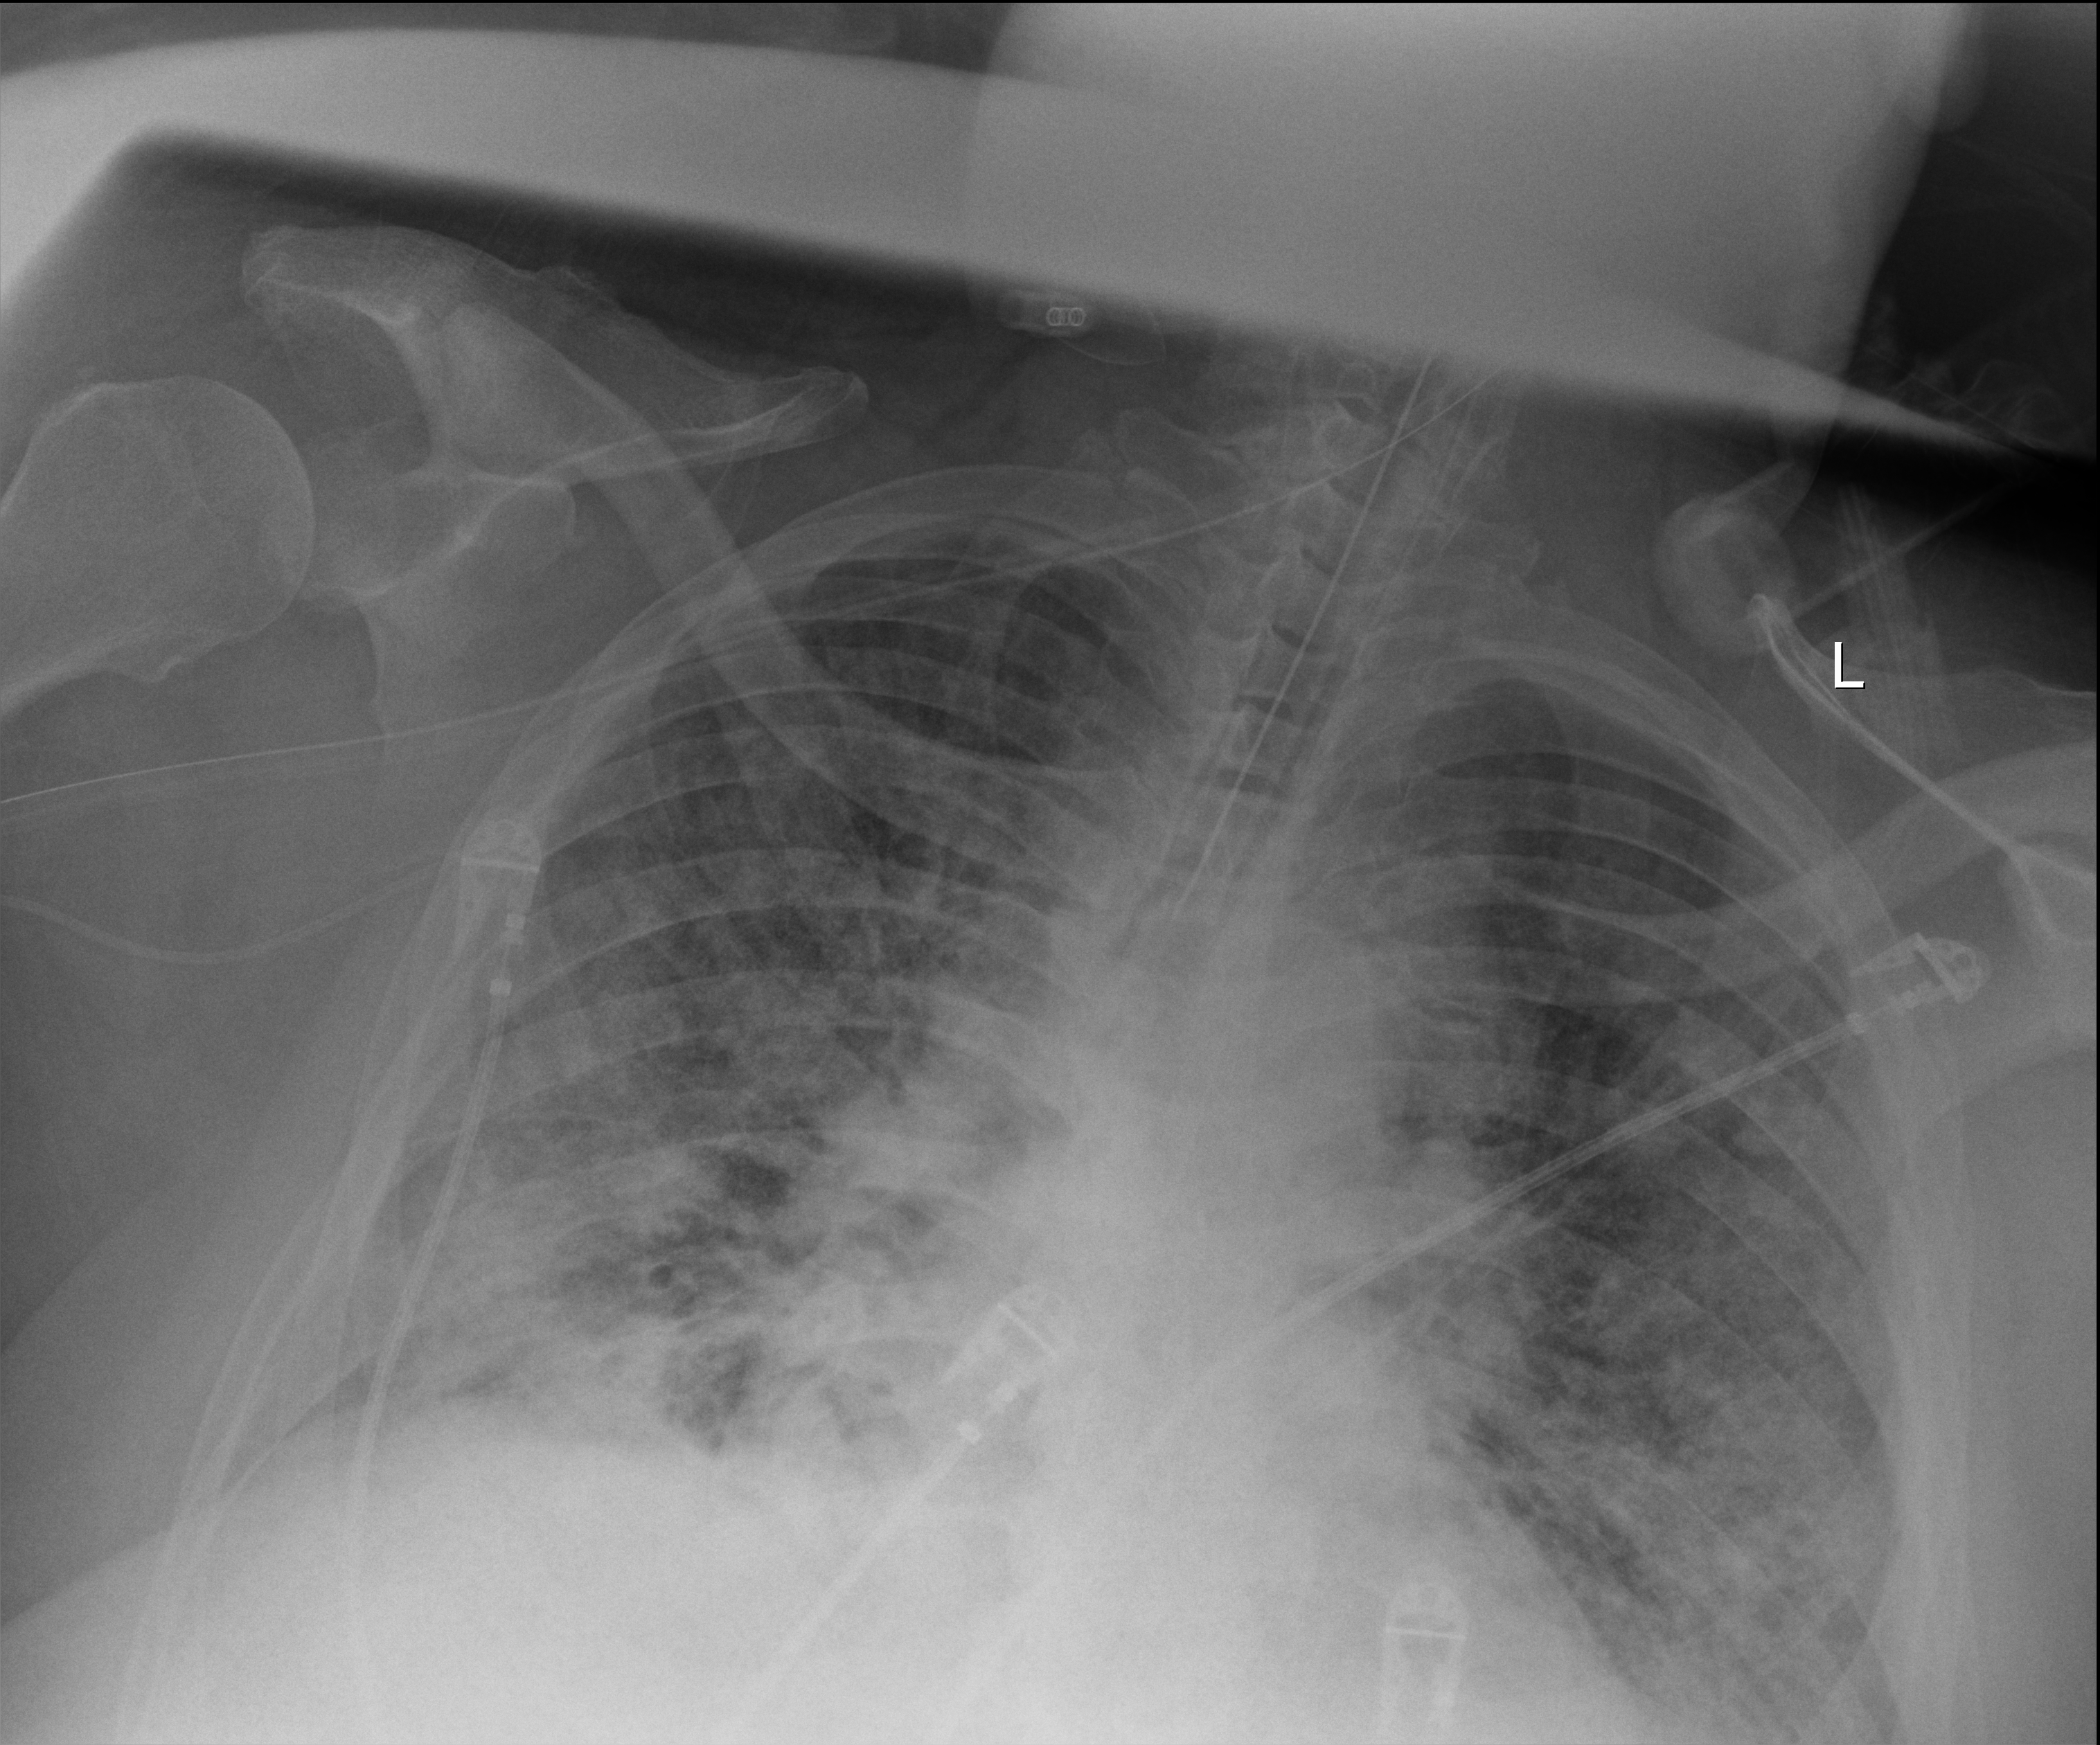
Portable chest radiograph; anteroposterior (AP) projection. Male patient hospitalised with COVID-19, age 60–74 years.
From the hospital-stay record, not from the radiograph (when in the stay this image was taken is not recorded):
- mechanically ventilated during this hospital stay: yes
- COPD (admission record): no
- admitted to intensive care during this hospital stay: yes